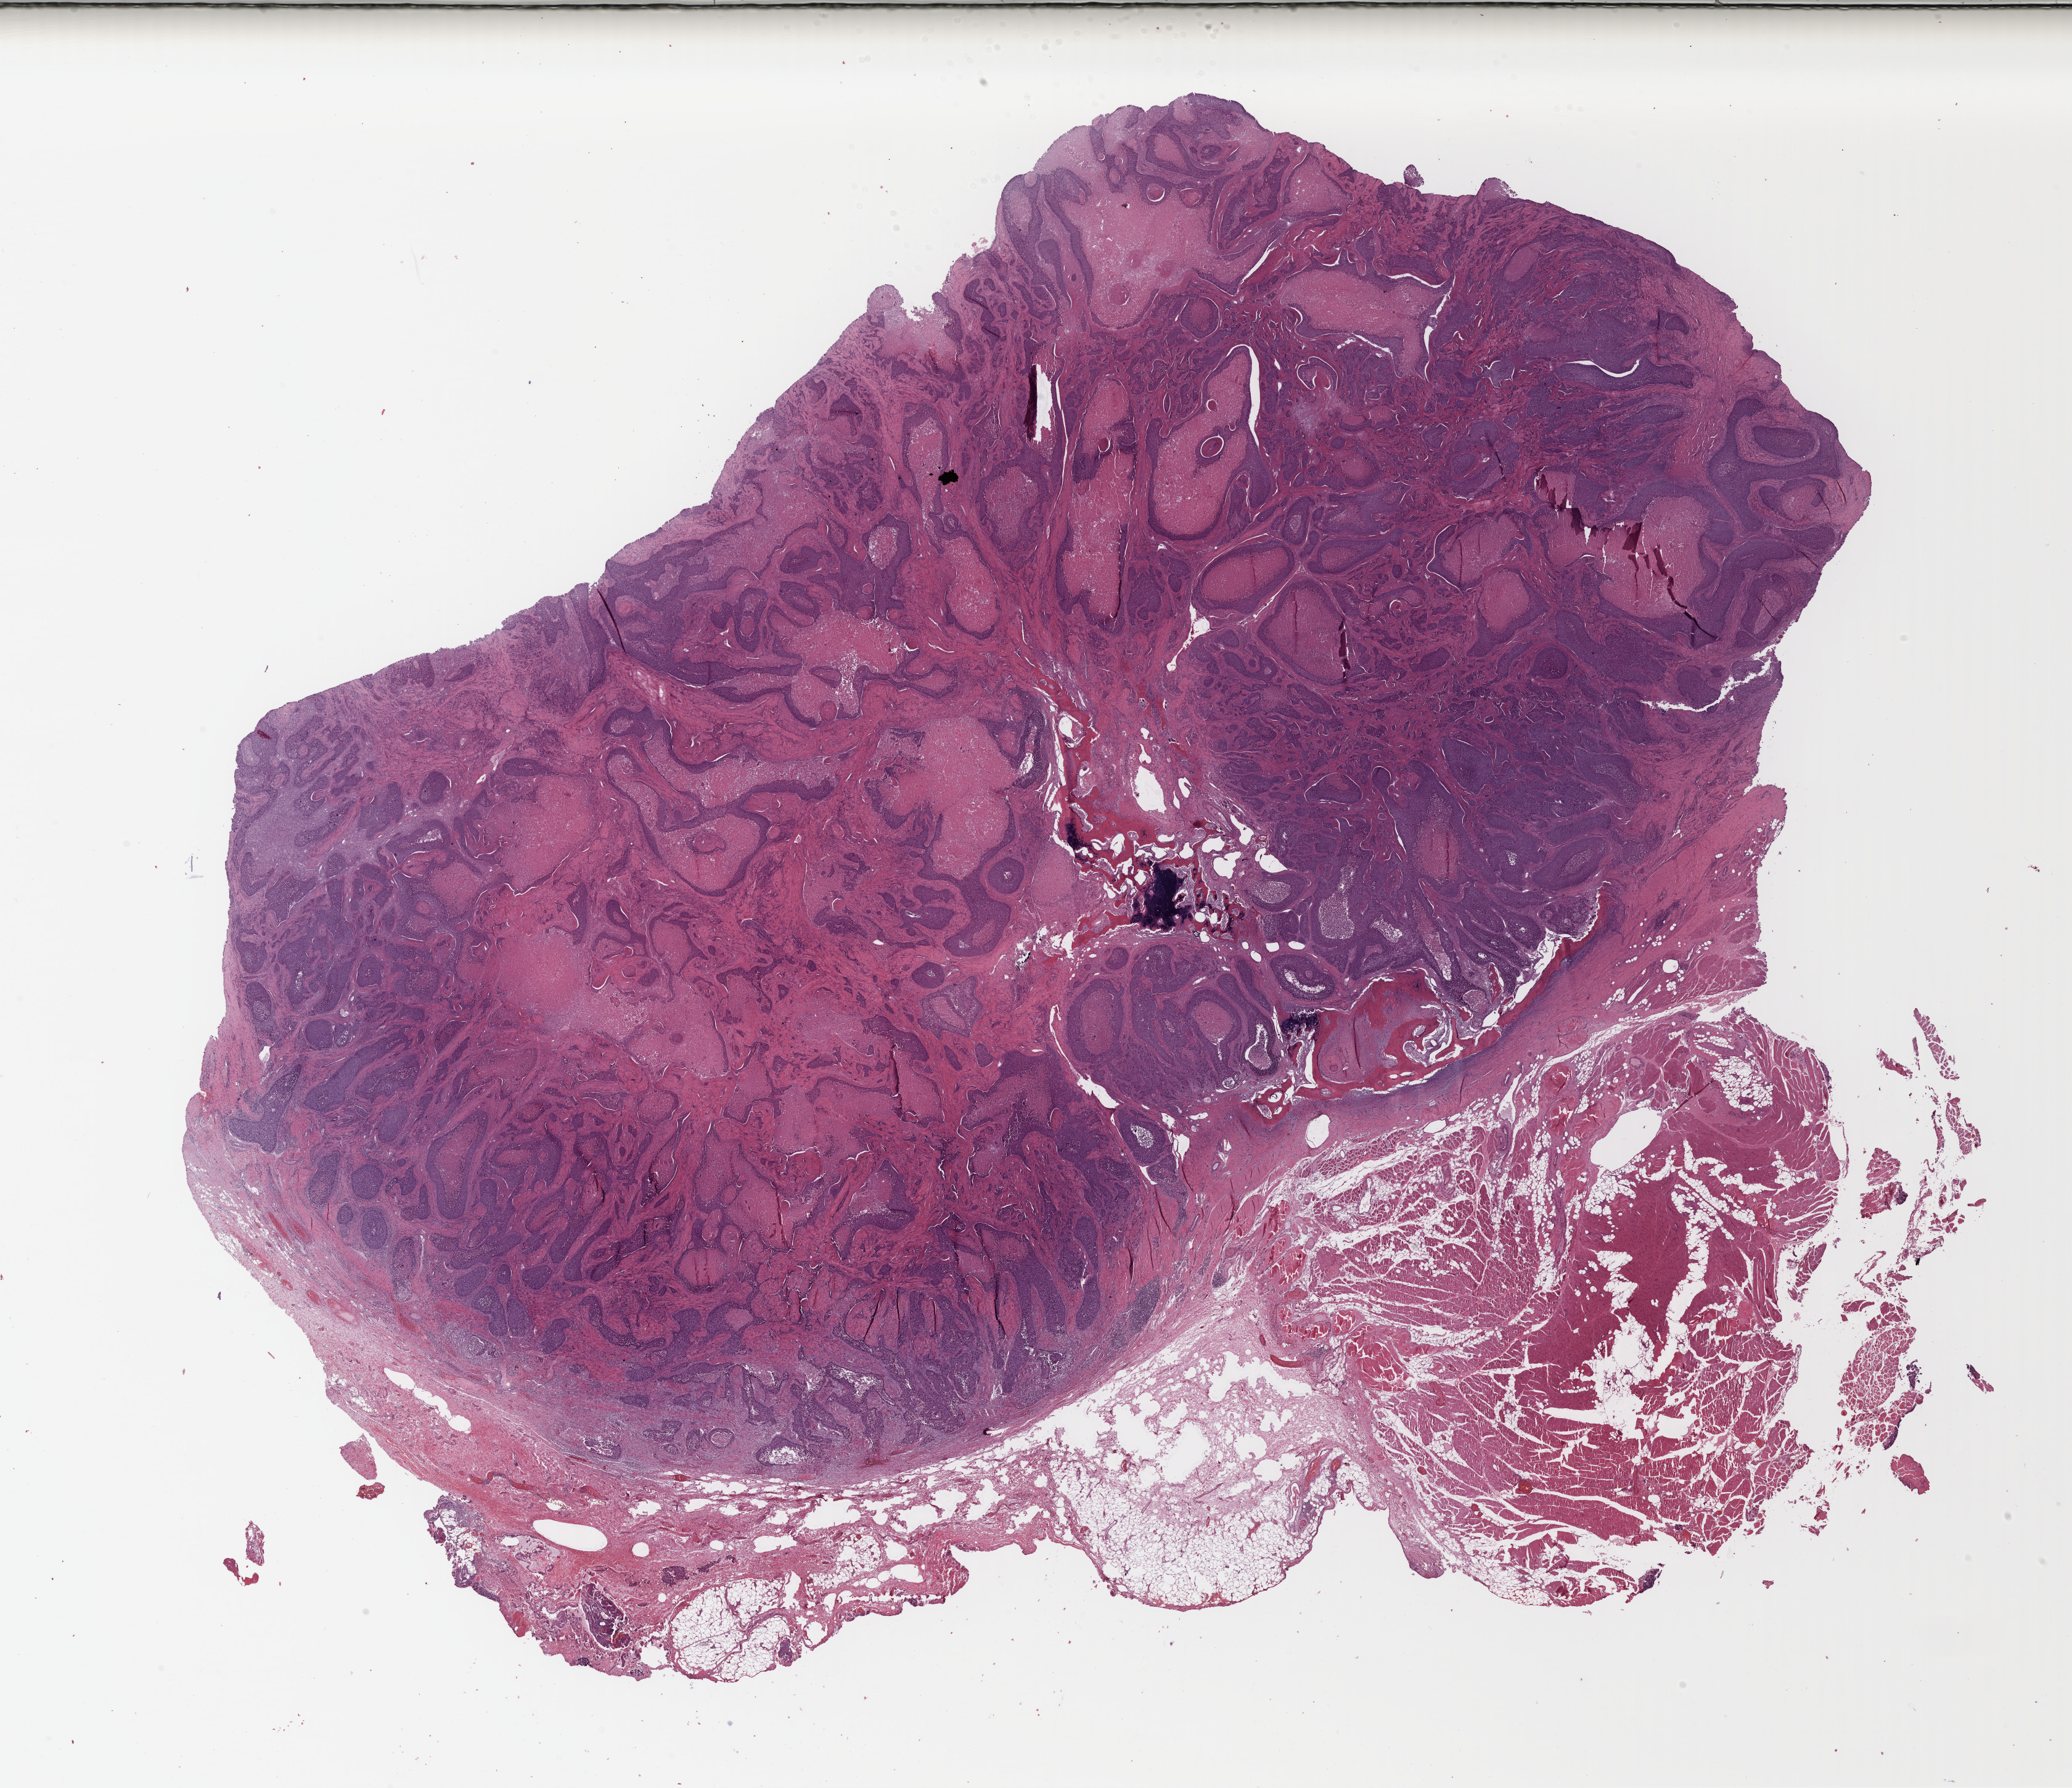
Hematoxylin and eosin (H&E) stained whole-slide image, low-resolution overview of the scanned area, about 26.4 x 22.8 mm (acquisition: 40x scan), formalin-fixed paraffin-embedded (FFPE) diagnostic section, lung, primary tumour sample. Female patient; age at initial diagnosis 45 years.
TNM: T3 N0 M0. AJCC pathologic stage: IIB. Pathologic diagnosis: Squamous cell carcinoma, NOS.